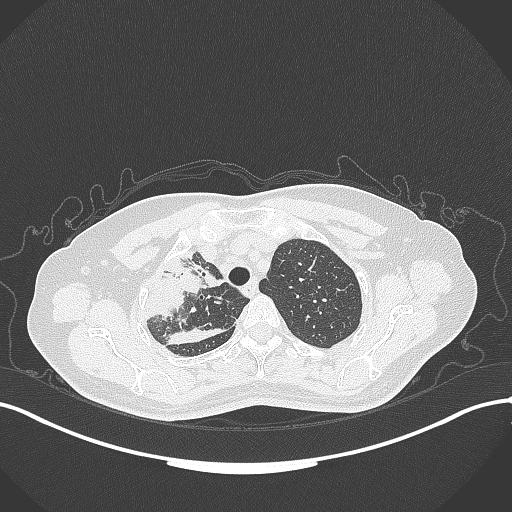
Chest CT, one axial slice. Position 260 of 309 along the scan axis. Reconstruction kernel B70f. 120 kVp. Lung window (W 1500 / L -600 HU). 512 × 512 image matrix. Patient: female, 60 years. From the clinical record (not read from this slice): clinical TNM (as recorded): T3 N1 M1.
Outlined on this slice (bounding box drawn by a radiologist):
- lung tumour (recorded histology: adenocarcinoma): bounding box (x1, y1, x2, y2) in pixels: (142, 243, 230, 326)